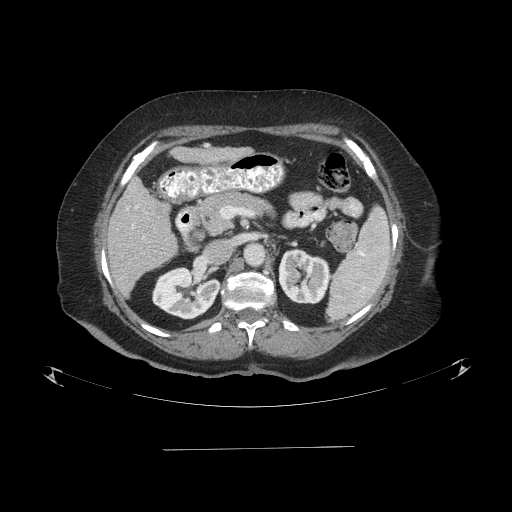
Contrast-enhanced abdominal CT (liver protocol), one axial slice. Position 40 of 103 along the scan axis. 120 kVp. One of 2 acquisitions stored at this slice position. Soft-tissue window (W 400 / L 40 HU). 2.5 mm slice thickness. 512 × 512 image matrix. Case-level facts recorded for this patient, not image findings: diagnosis: hepatocellular carcinoma (patient treated with transarterial chemoembolisation; whether this scan precedes or follows treatment is not stated here); TNM stage (as recorded): Stage-IIIA; Child-Pugh class: A.
Structures marked on this image (semi-automatic segmentation, software-assisted and operator-edited):
- liver parenchyma outside the tumour (the mass and vessels are separate outlines, so this box may not span the whole liver): bounding box <108,178,176,296> (left, top, right, bottom; pixels)
- liver vessels: <126,206,144,238>